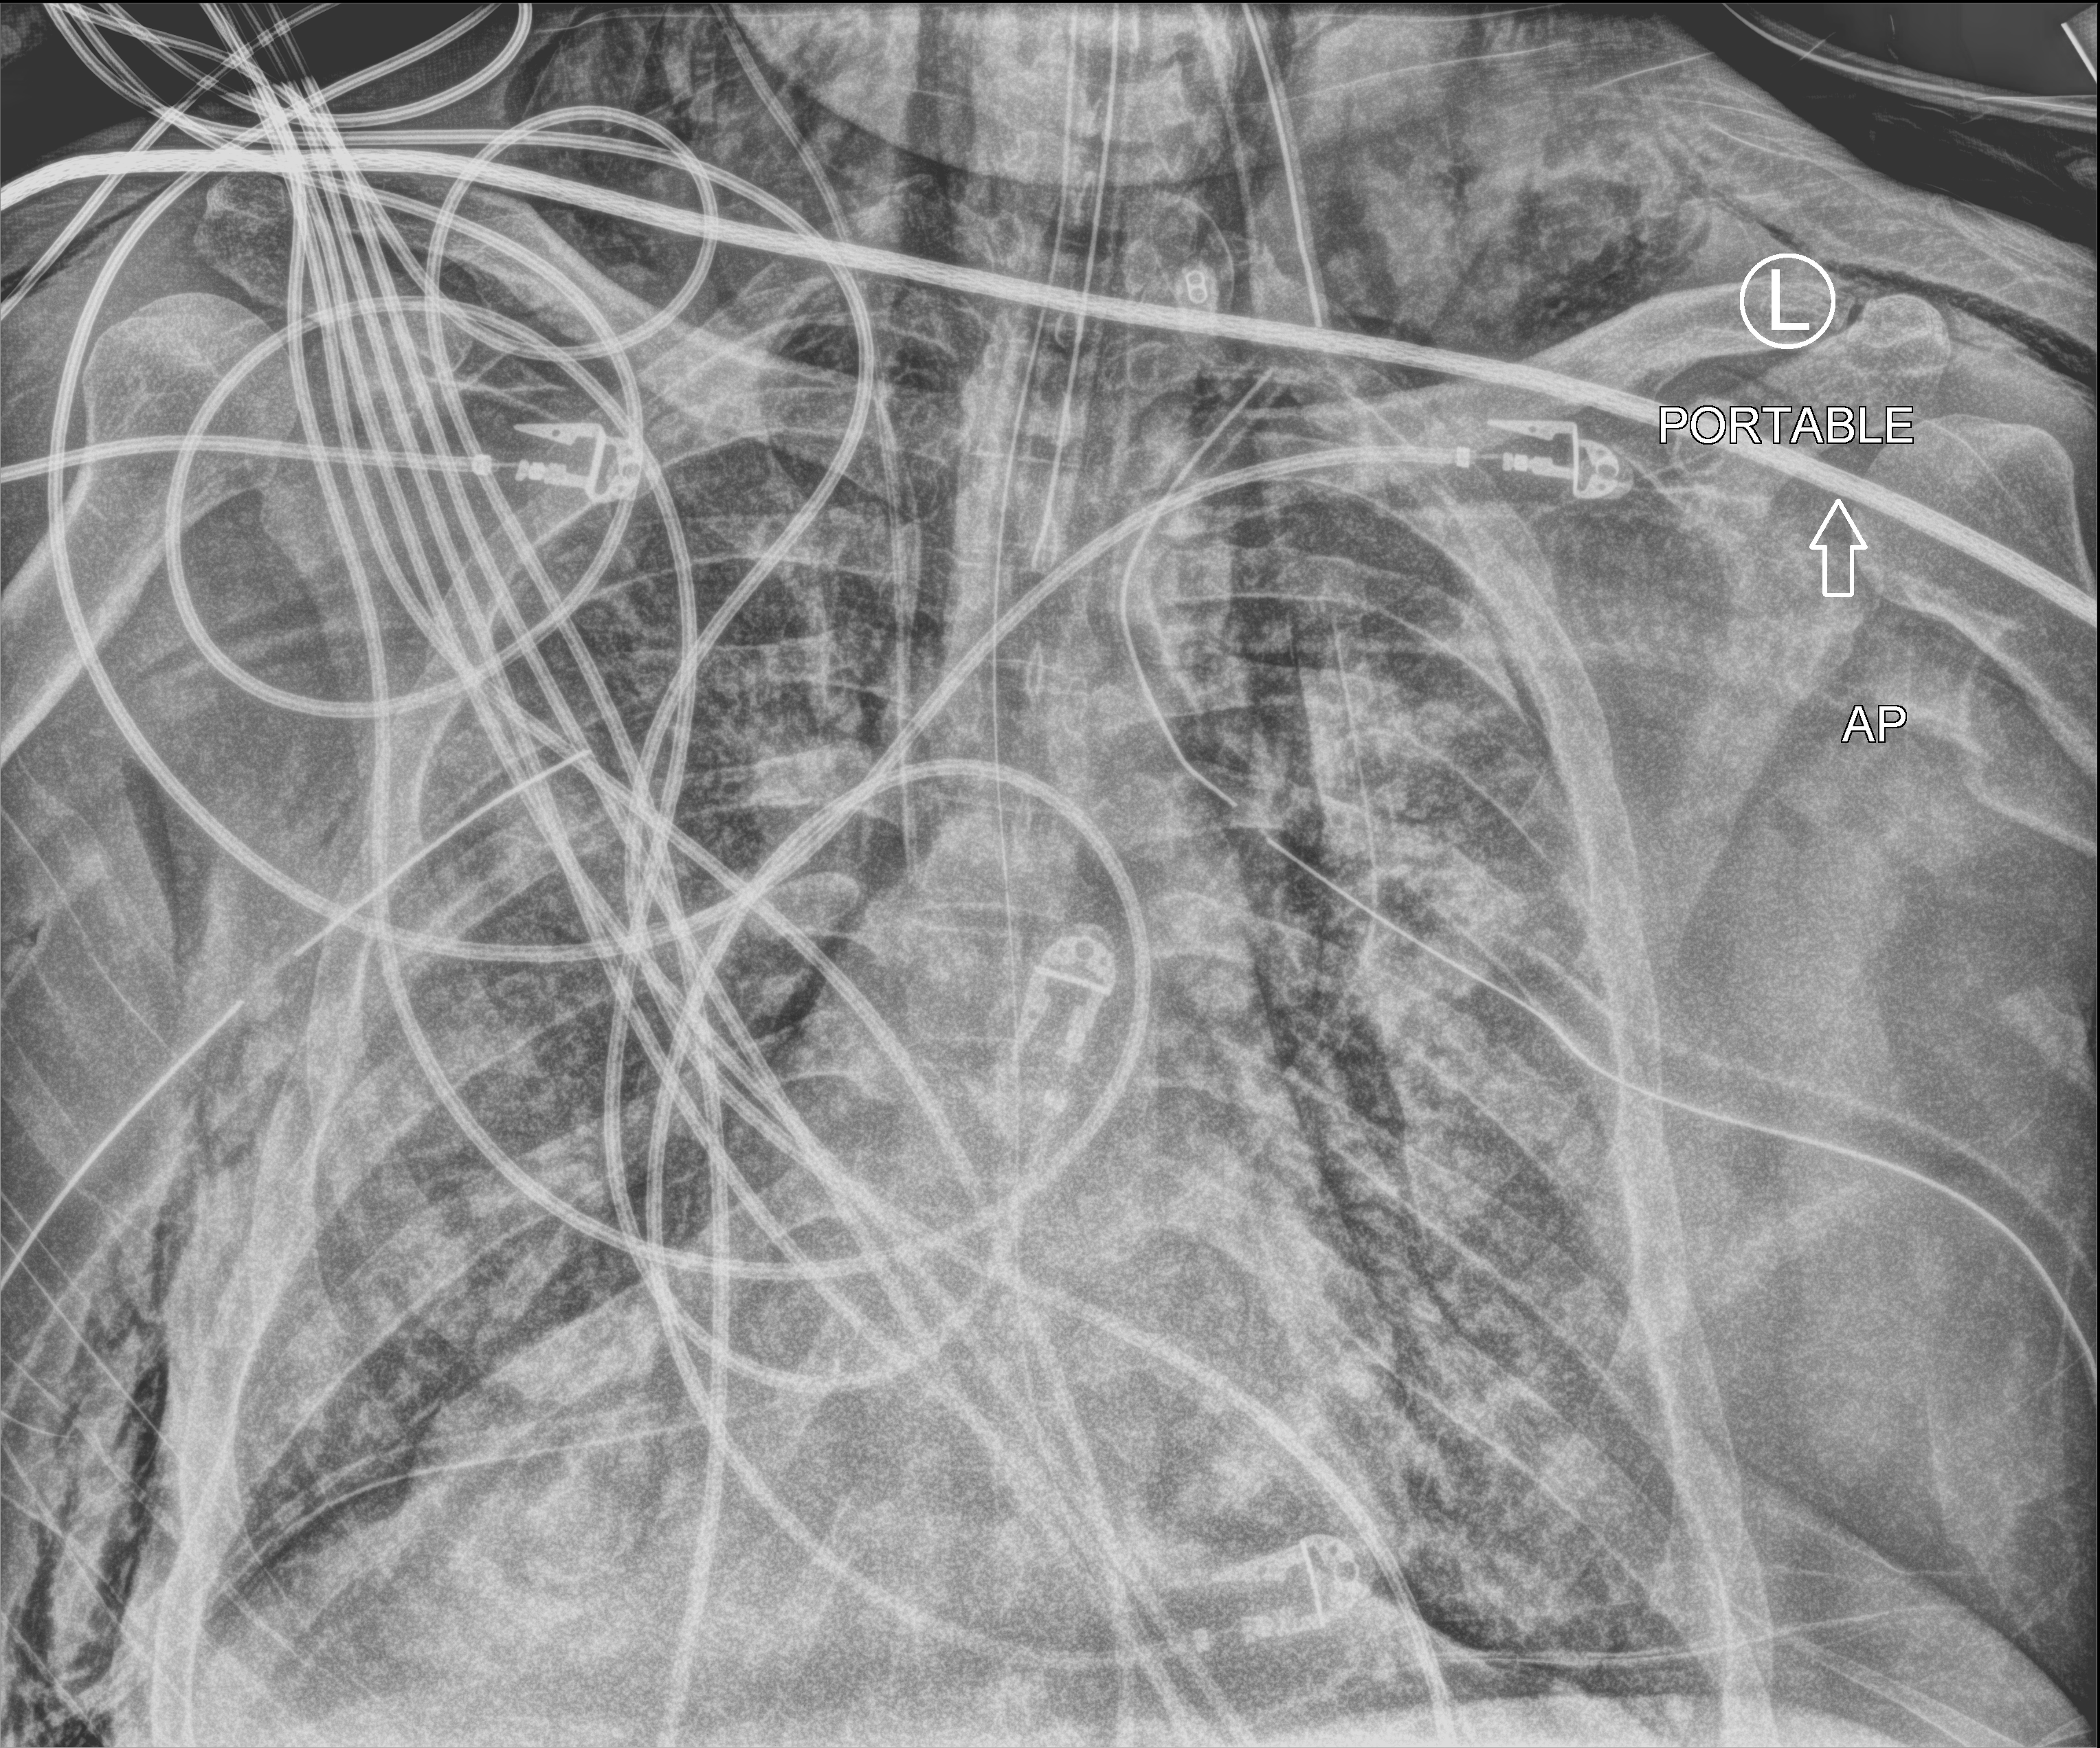
Bedside chest radiograph (computed radiography); anteroposterior (AP) projection. Patient hospitalised with COVID-19, aged 18–59 years.
Hospital-stay facts (about this admission, not read from this image; timing relative to this image not recorded):
- admitted to intensive care during this hospital stay: yes
- hypertension (admission record): no